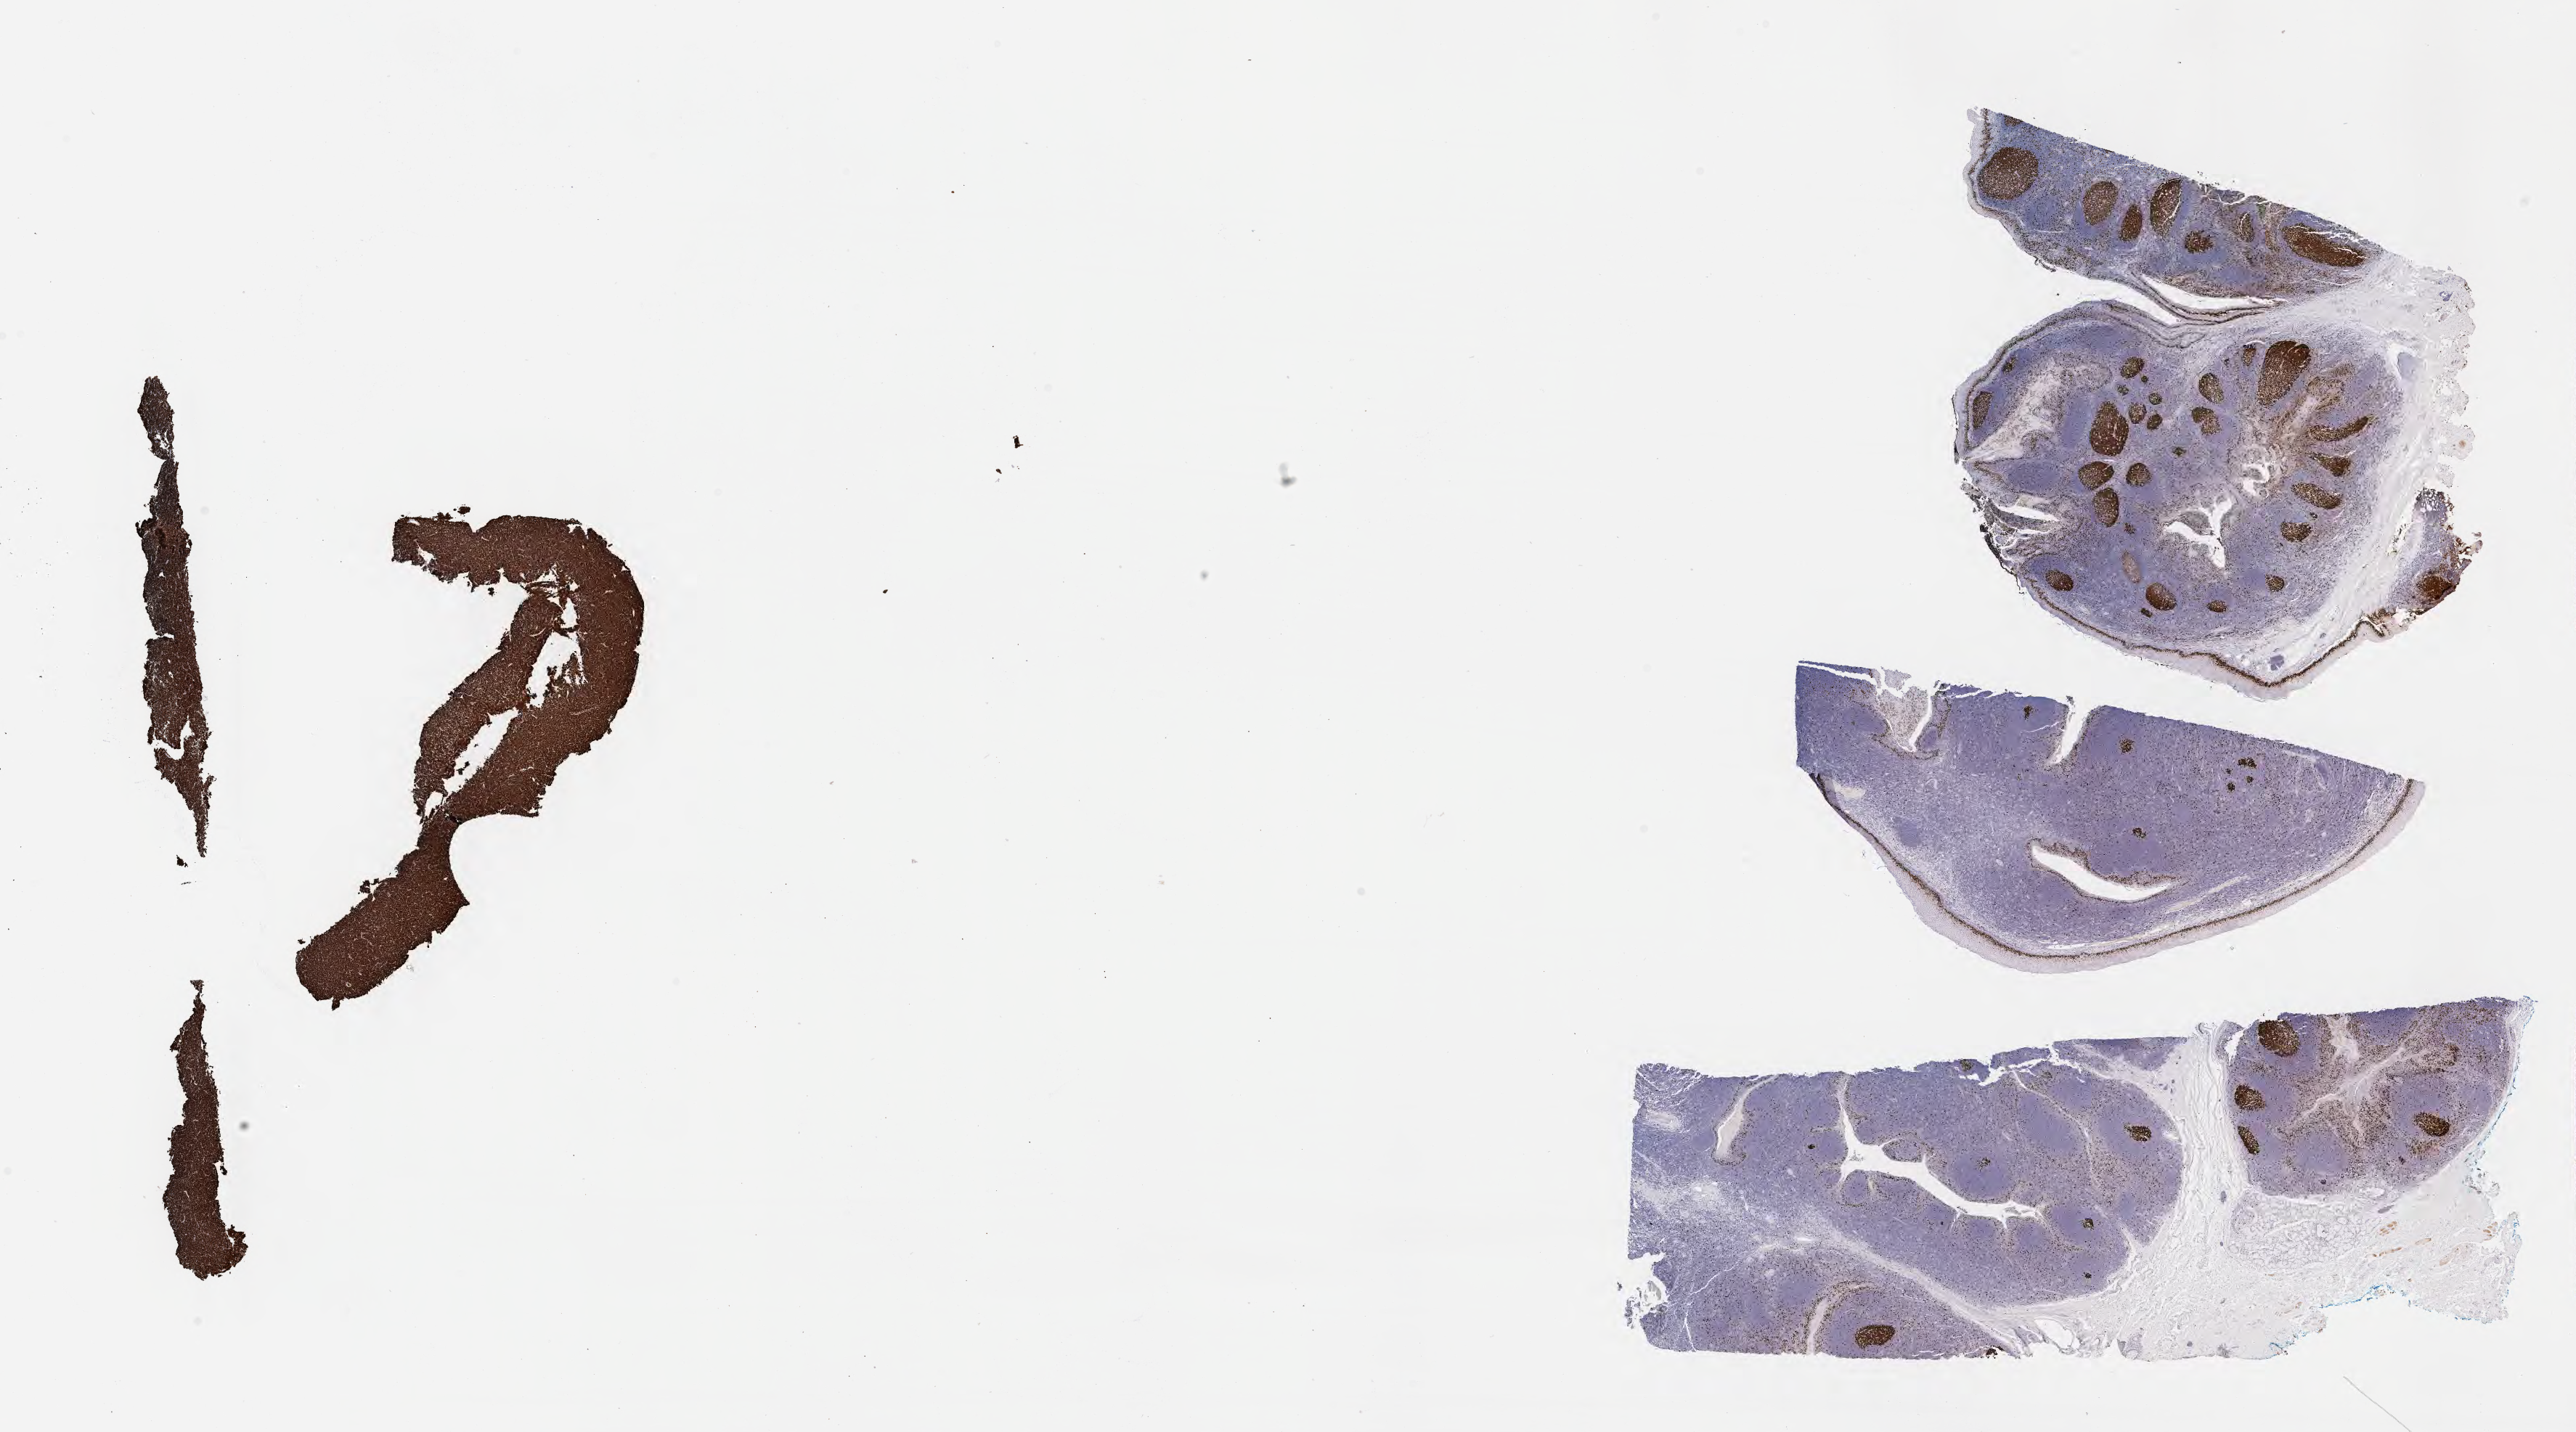
Whole-slide image, immunohistochemical stain for Ki-67, shown as a low-resolution overview of the whole scanned area (about 28.7 x 15.9 mm). Tumor tissue. Anatomic site: peritoneum. Female patient; age at initial diagnosis 7 years.
Diagnosis: Burkitt lymphoma, NOS.